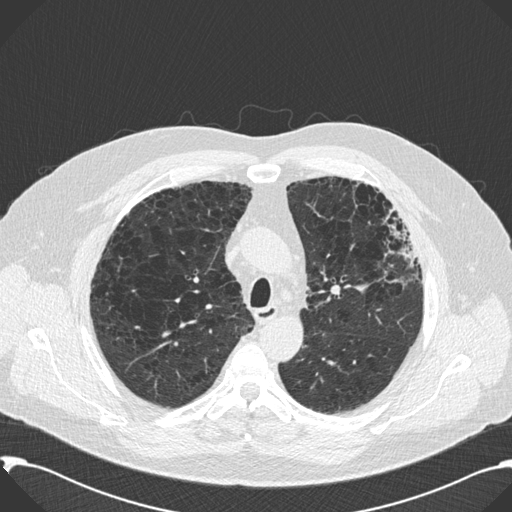
Axial slice from a low-dose chest CT screening exam. Second screening round (one year after baseline). Lung window (W 1500 / L -600 HU). 2 mm slice thickness. Slice 50 of 199 in the series. Male participant, aged 59 years at enrolment. Current smoker at enrolment.
Expert reader's lesion annotation, bounding box (x1, y1, x2, y2) in pixels: (362, 201, 424, 294). No non-calcified nodule or mass ≥4 mm was recorded by the screening reader at this exam. Later outcome: lung cancer diagnosed 518 days after this screen — bronchiolo-alveolar carcinoma, mixed mucinous and non-mucinous, left upper lobe, stage IA (AJCC 6th edition), 20 mm at pathology.